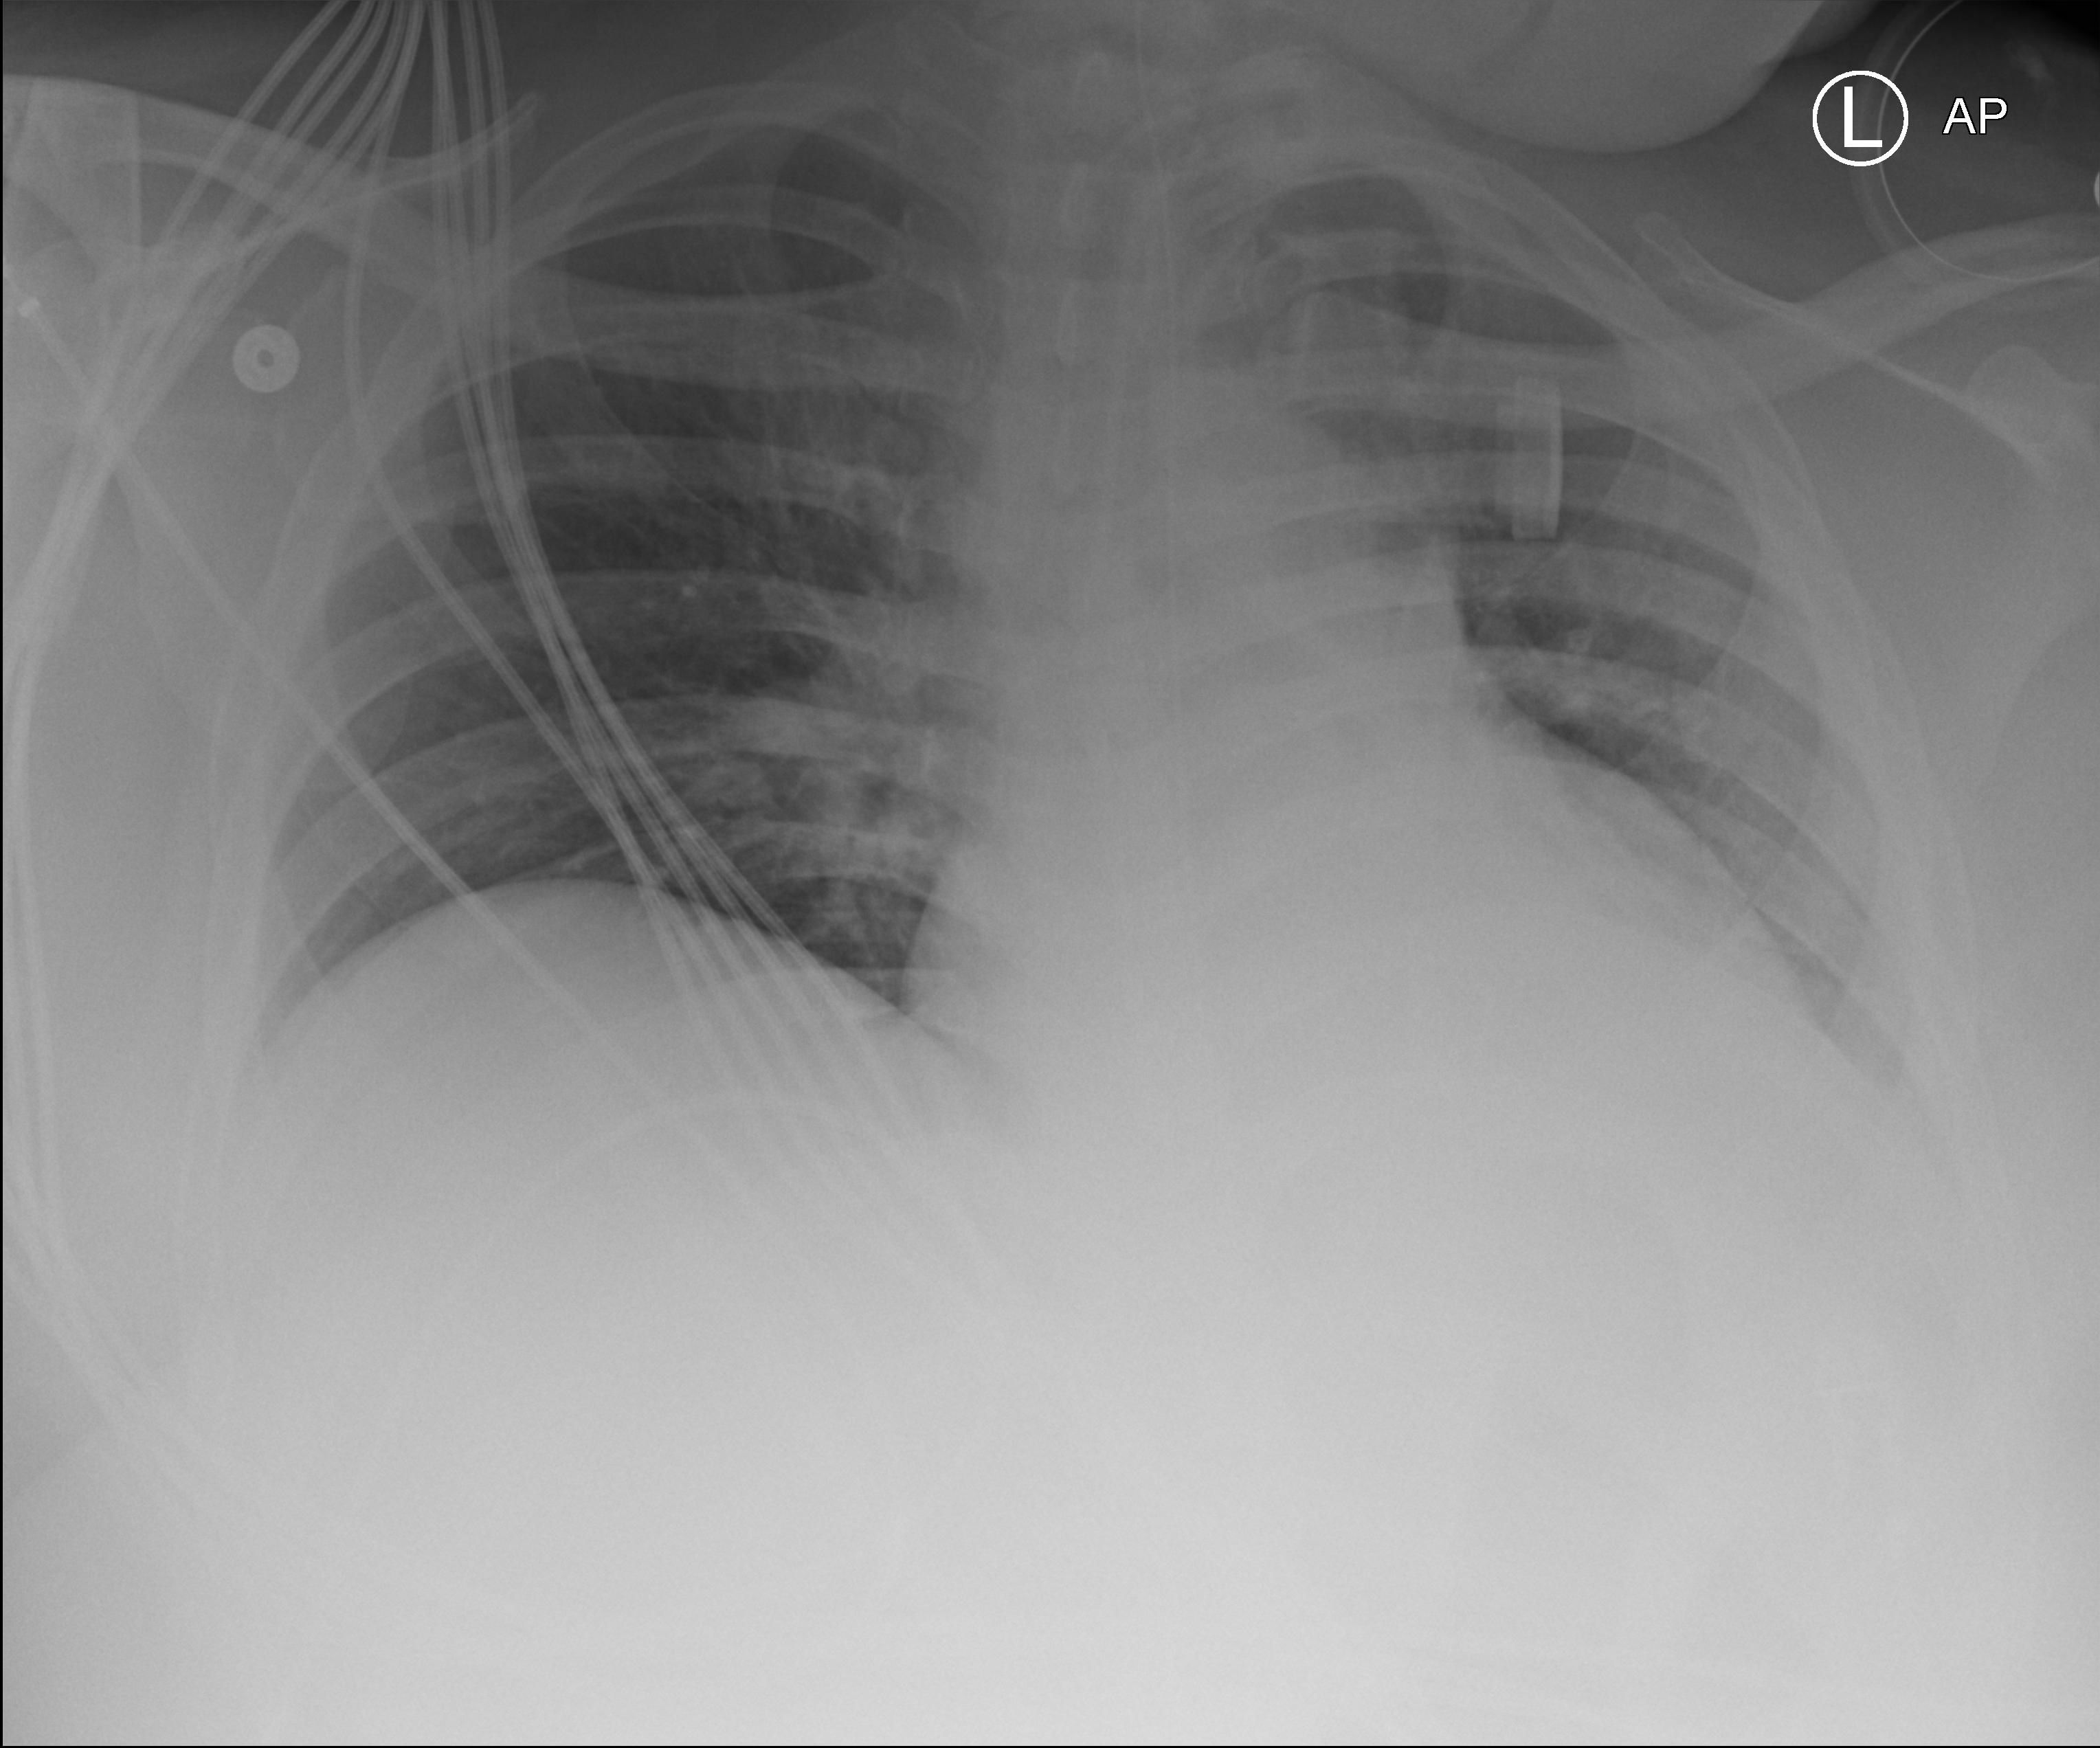
Portable chest radiograph, anteroposterior (AP) projection. Male patient hospitalised with COVID-19, age 18–59 years.
Hospital-stay facts (about this admission, not read from this image; timing relative to this image not recorded): other chronic lung disease (admission record): yes.